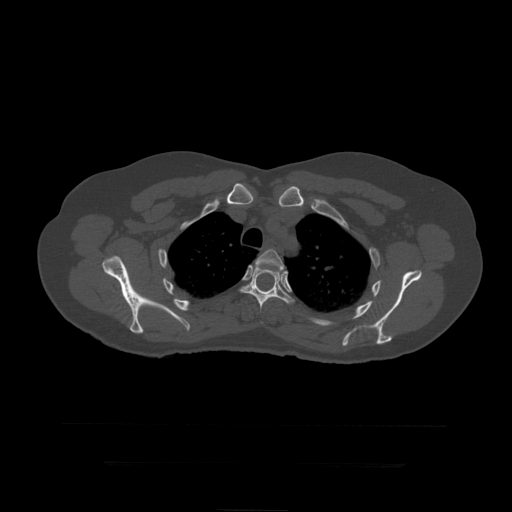
CT including the spine, one axial slice; slice 339 of 399 in the series (ordered by position); reconstruction kernel STANDARD; 120 kVp; bone window (W 1800 / L 400 HU); 1.25 mm slice thickness; 512 × 512 image matrix, field of view 450 × 450 mm. Patient age 41 years. From the clinical record (not read from this slice): primary cancer: breast.
Outlined on this slice (semi-automatic segmentation, software-assisted and operator-edited):
- T4 vertebra: box from (x=254, y=249) to (x=284, y=273) px
- T5 vertebra: (x=240, y=268)–(x=295, y=323)